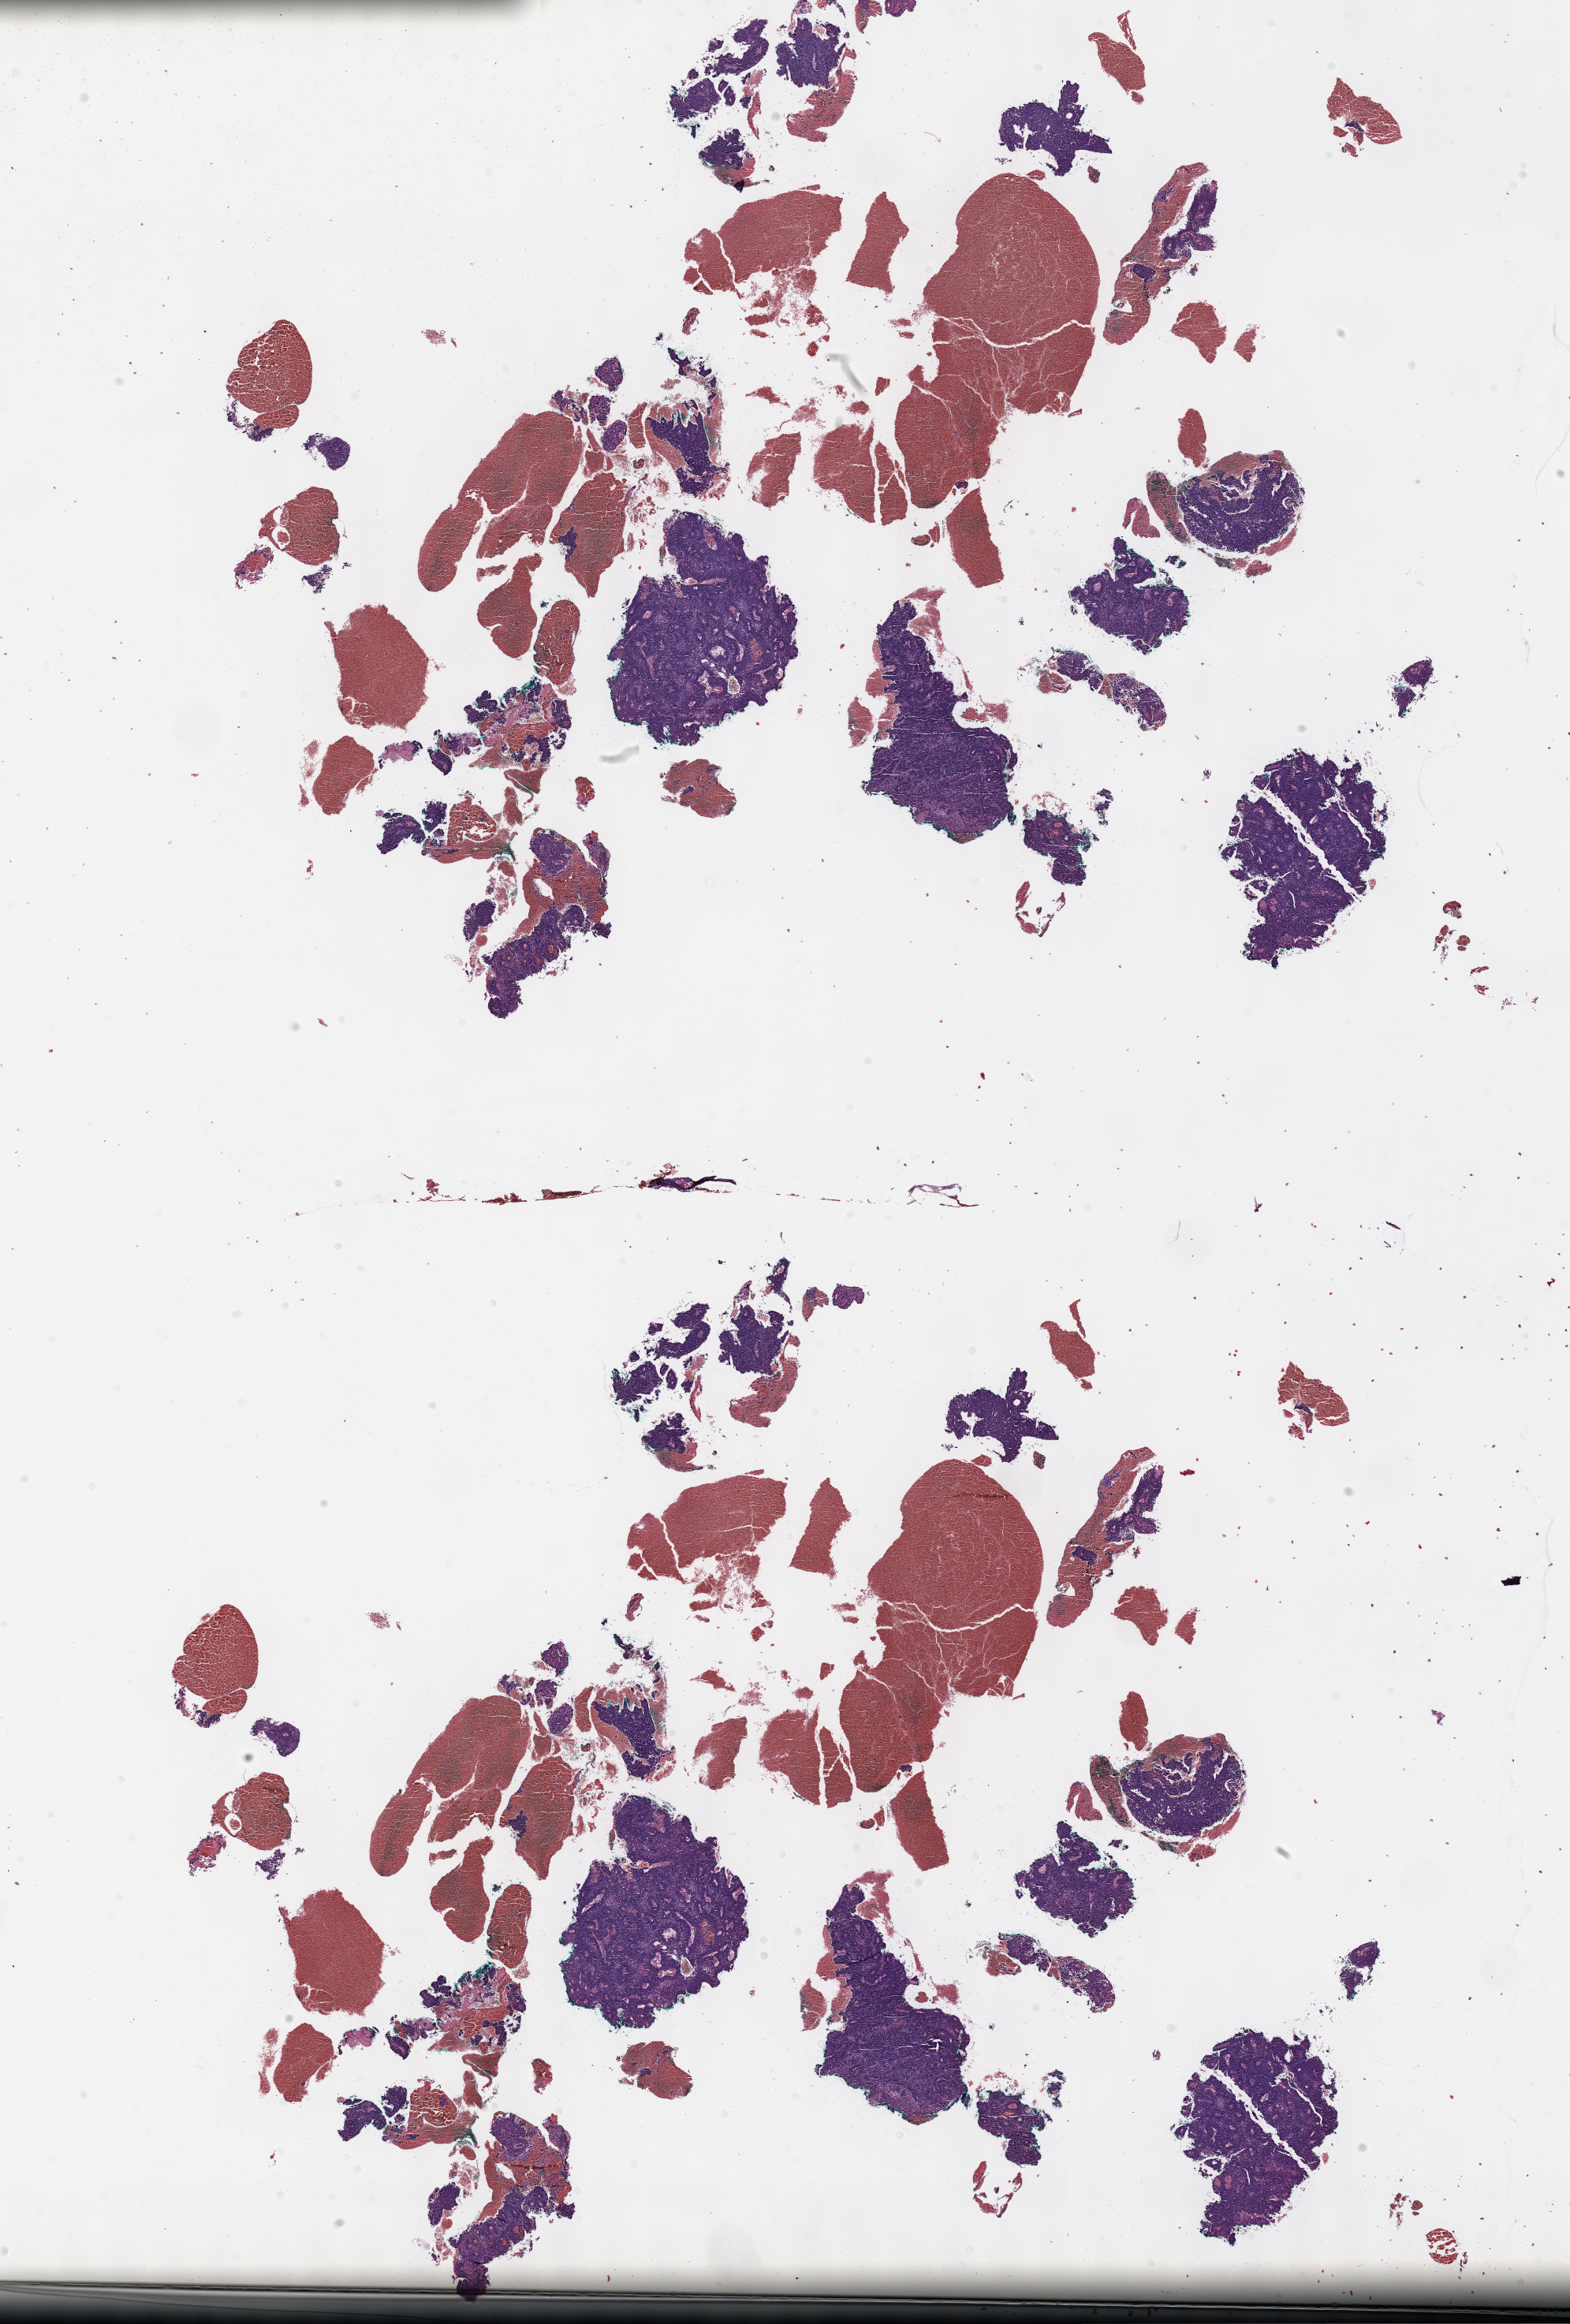
Whole-slide histology image, H&E — shown as a low-resolution overview of the whole scanned area (about 16.1 x 23.8 mm), FFPE section, primary tumour sample from the cervix. Patient: female, age at initial diagnosis 64 years. Histologic grade: G3 (poorly differentiated).
Pathologic diagnosis: Squamous cell carcinoma, NOS. FIGO stage: IB1.